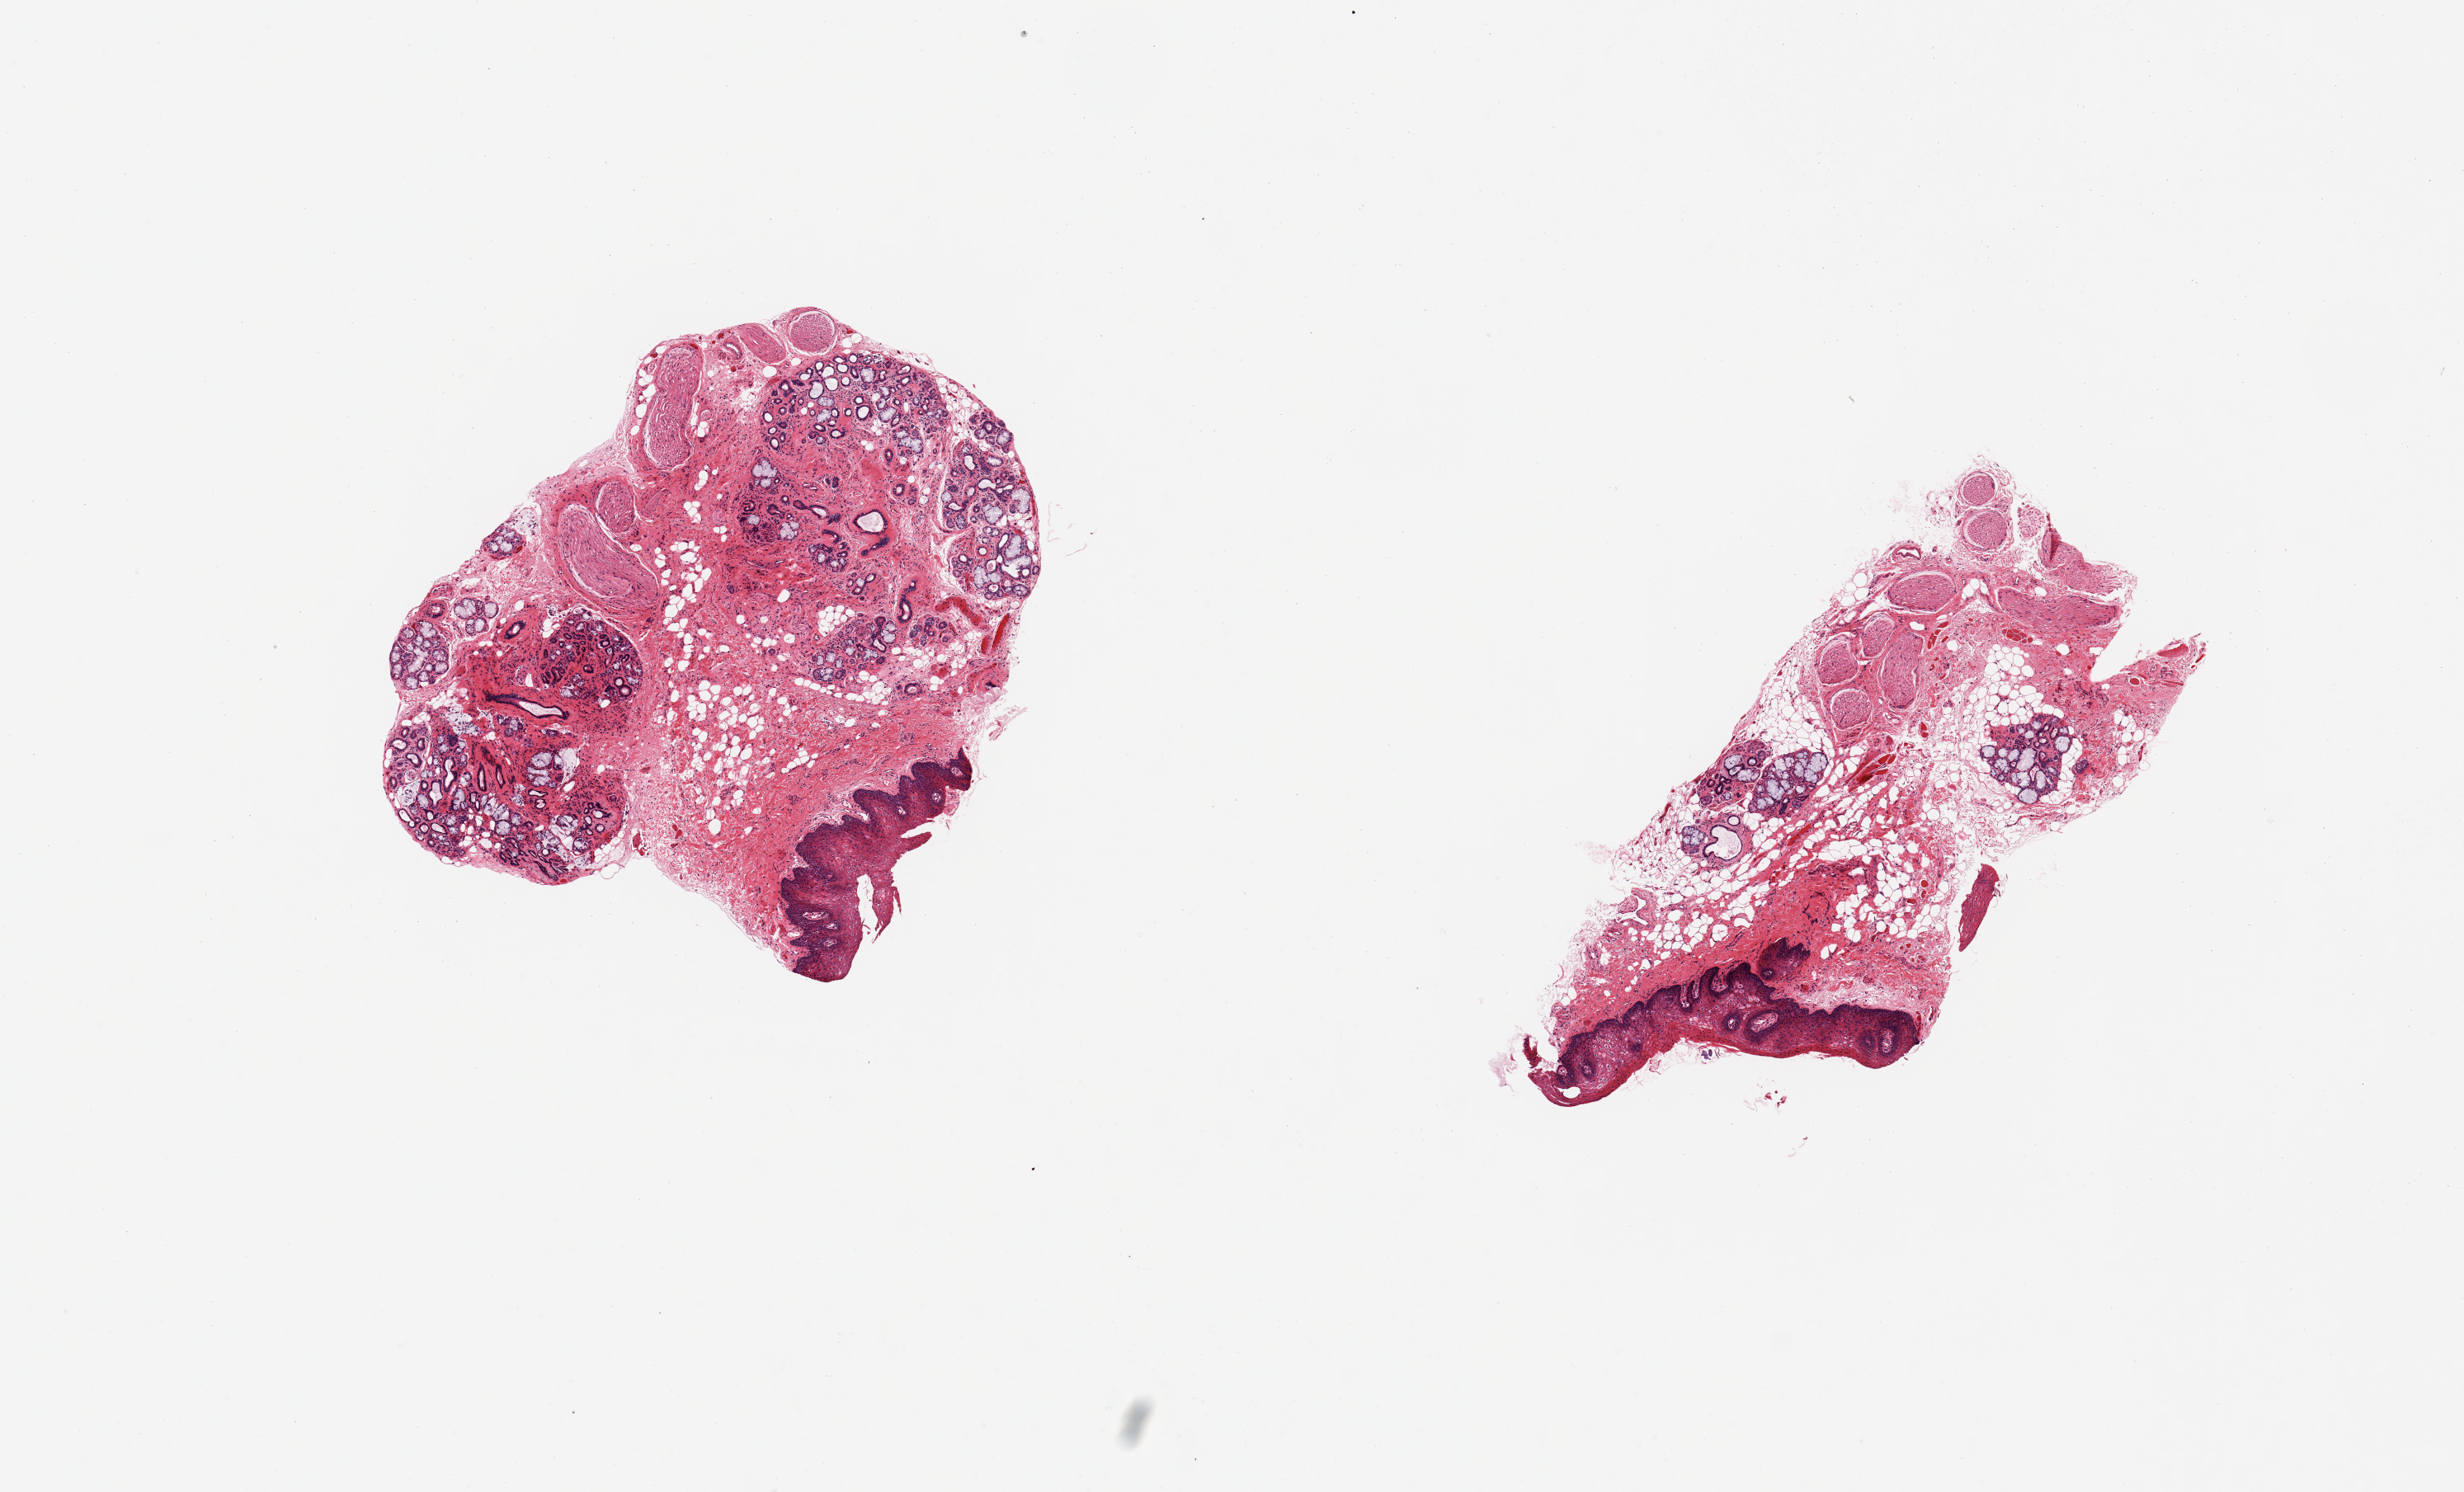
Digitized haematoxylin and eosin-stained section — whole scanned area (about 11.8 x 7.2 mm, acquisition: 20x scan) shown as a low-resolution overview. Donor sex: female.
Specimen: PAXgene-fixed paraffin-embedded (PFPE) section; target tissue: minor salivary gland; donor tissue sample.